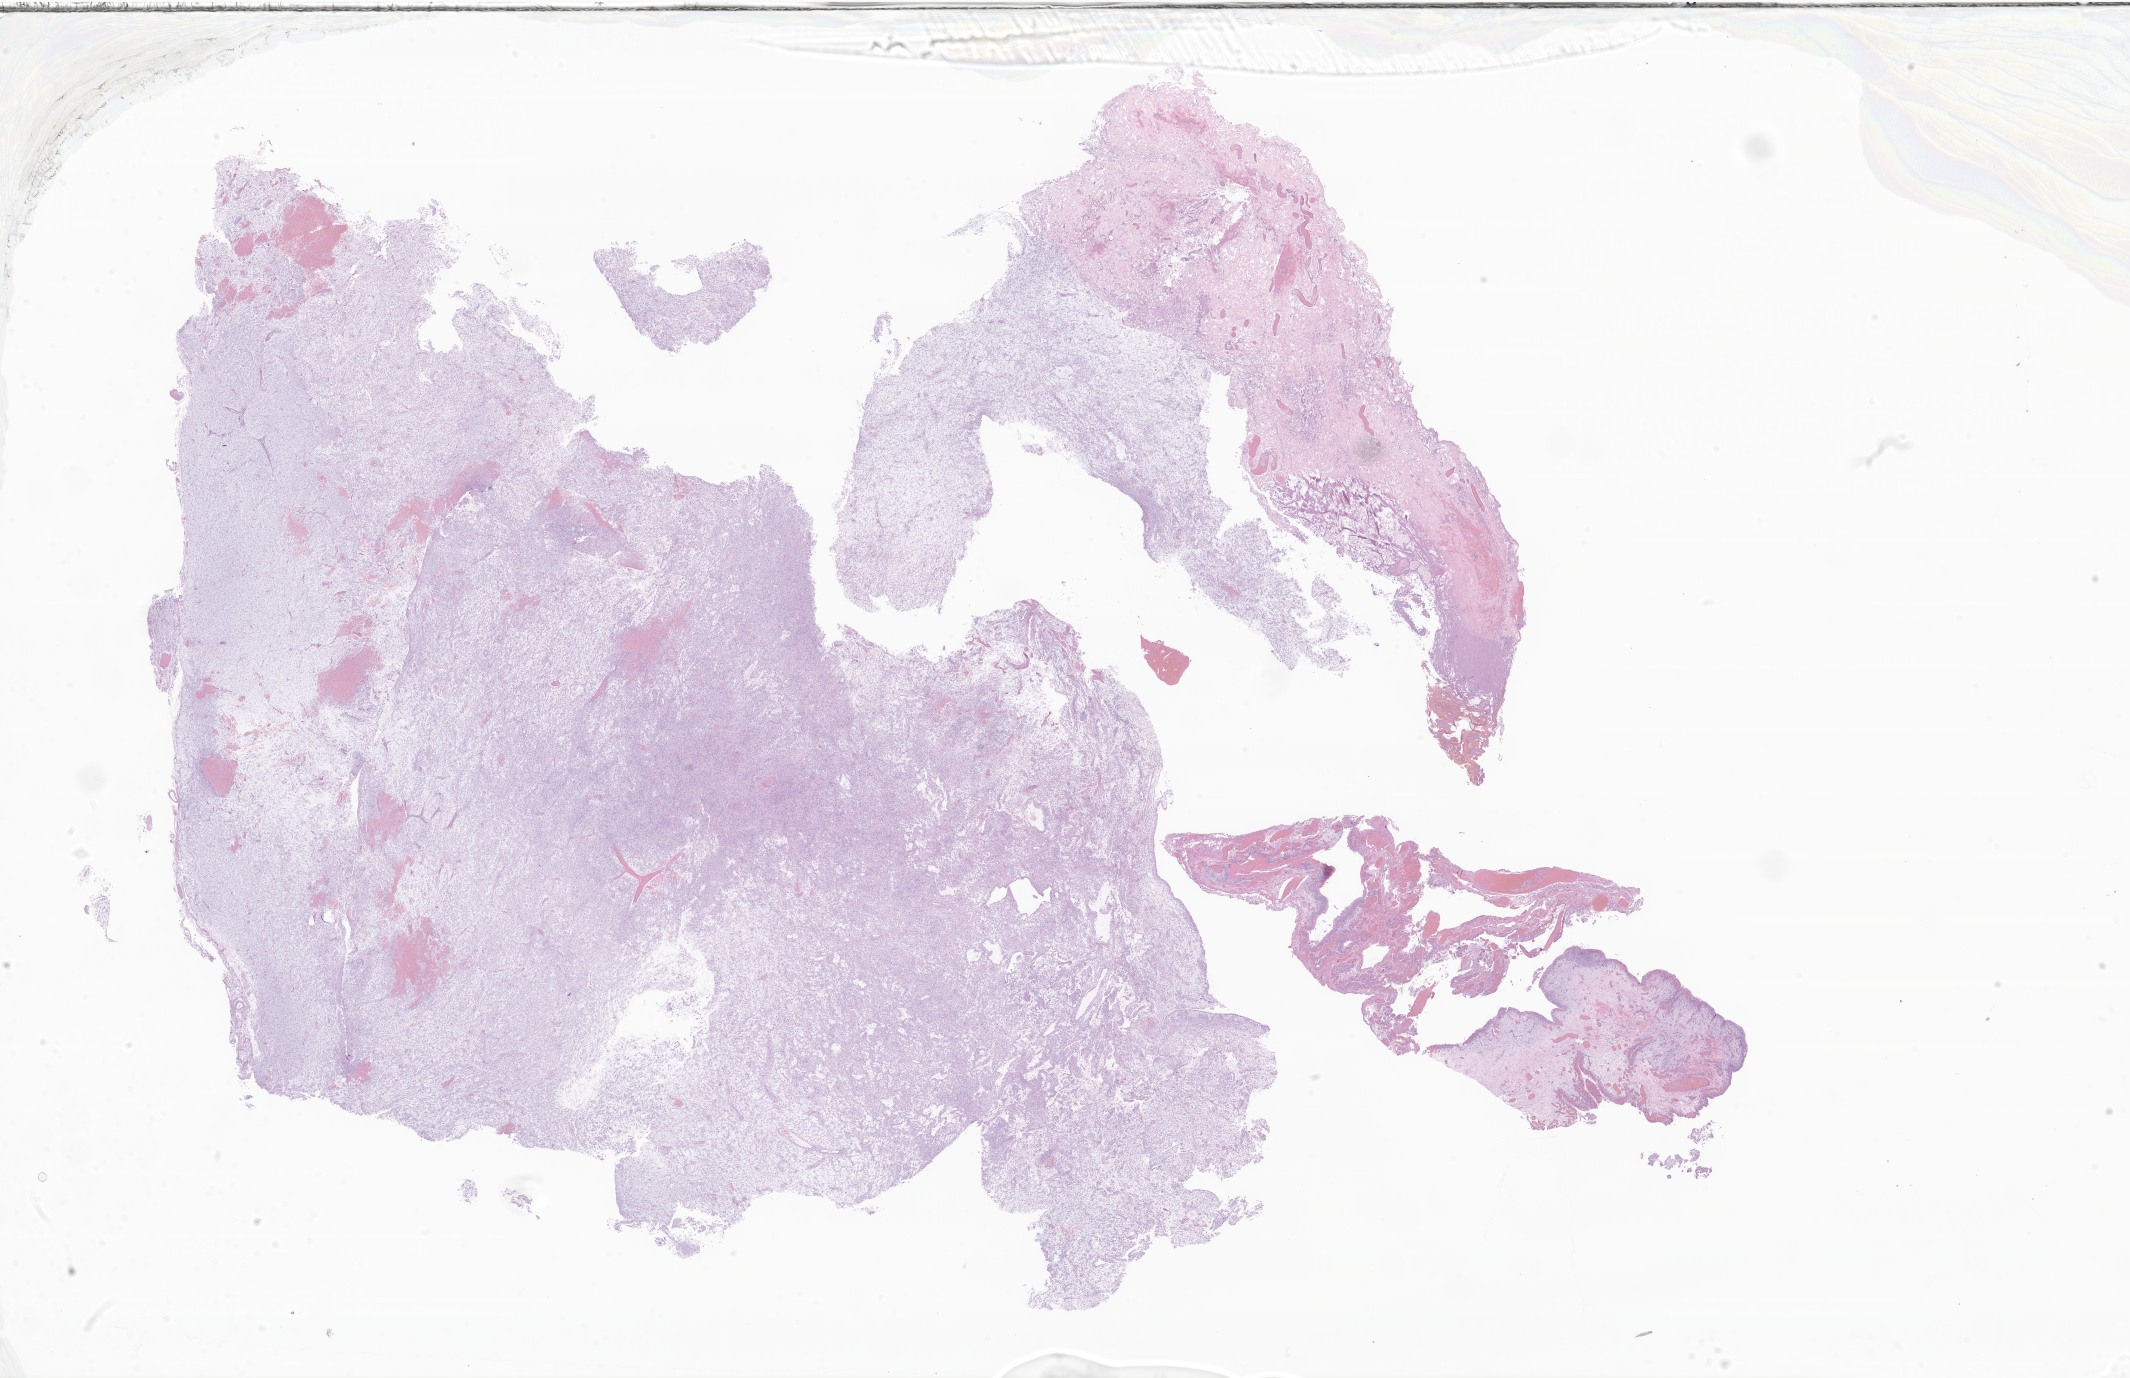
Whole-slide image, H&E stain of tumor tissue from the cerebellum, whole scanned area (about 35.9 x 23.2 mm) shown as a low-resolution overview. FFPE section. Patient female; age 70 months (5 years 10 months).
Diagnosis (ICD-O-3 morphology term): Pilocytic astrocytoma.